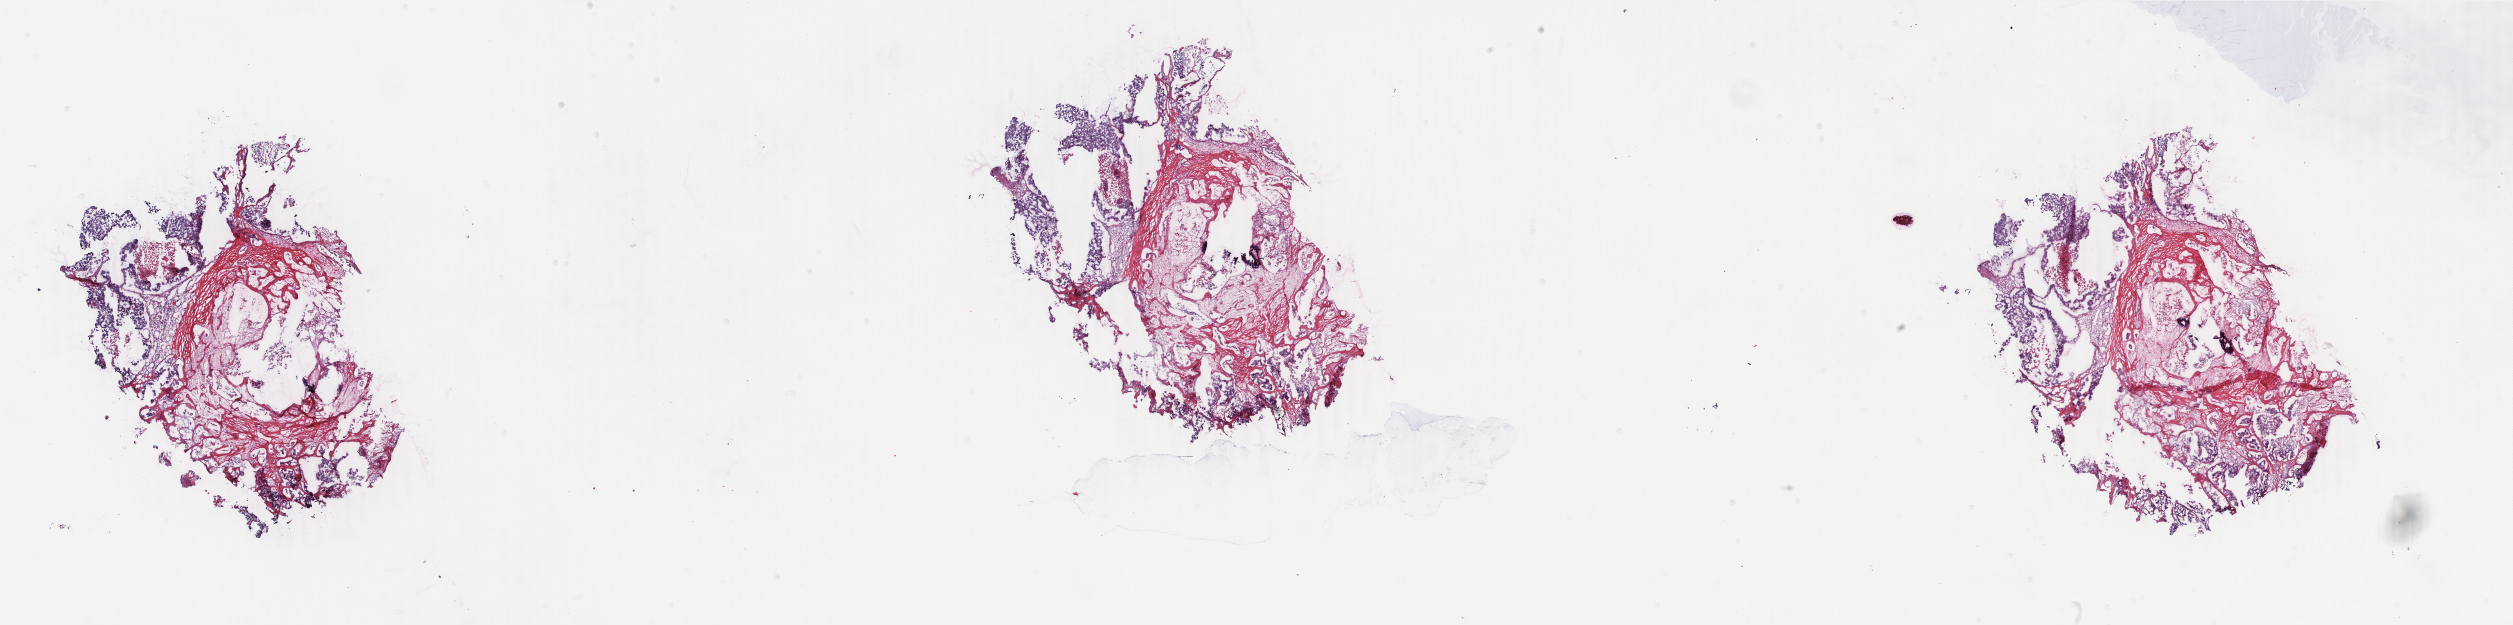
H&E whole-slide image, a low-resolution overview of the entire scanned area, about 40.0 x 9.9 mm. Frozen section. Primary tumour sample from the breast. Female, age 73 years at initial diagnosis. Slide review estimates, as recorded: tumour cells 60%, tumour nuclei 65%, normal cells 0%, stromal cells 25%, necrosis 15%. Inflammatory infiltration, as recorded: lymphocyte infiltration 1%, monocyte infiltration 0%, neutrophil infiltration 0%.
Laterality: left. Lymph nodes positive (case pathology): 0 of 7 examined. Histologic diagnosis: Infiltrating duct carcinoma, NOS. TNM: T2 N0 M0. AJCC pathologic stage: IIA (5th edition).